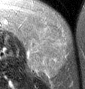
MRI of an extremity soft-tissue mass, one axial slice. Position 15 of 46 along the scan axis. T2-weighted fat-saturated. MR volume resampled by the dataset authors to the PET/CT grid (not the native acquisition matrix). 85 × 89 image matrix. Female patient. Case-level facts recorded for this patient, not image findings: histological type: leiomyosarcoma; grade: intermediate; site of the primary tumour: parascapusular.
Outlined on this slice (expert contour drawn on MRI and transferred to this co-registered scan by the dataset authors):
- gross tumour volume including surrounding oedema: box from (x=27, y=25) to (x=67, y=79) px
- gross tumour volume (mass): (x=27, y=25)–(x=67, y=77)